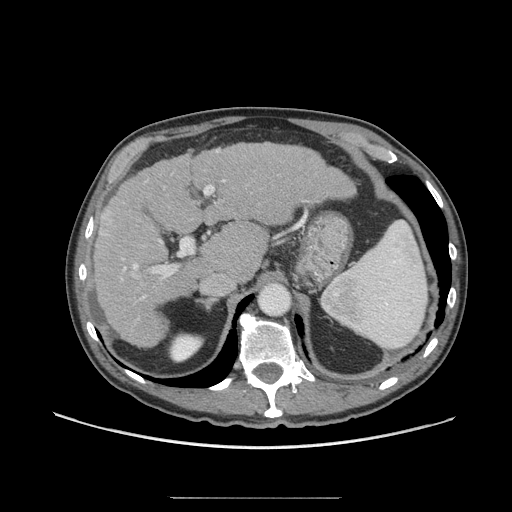
Contrast-enhanced abdominal CT (liver protocol), one axial slice; slice 44 of 71 in the series (ordered by position); 140 kVp; soft-tissue window (W 400 / L 40 HU); 512 × 512 image matrix, field of view 400 × 400 mm. From the clinical record (not read from this slice): diagnosis: hepatocellular carcinoma (patient treated with transarterial chemoembolisation; whether this scan precedes or follows treatment is not stated here); TNM stage (as recorded): Stage-I; Child-Pugh class: A; tumour differentiation: well differentiated; tumour nodularity: uninodular.
Annotated regions visible in this slice (semi-automatic segmentation, software-assisted and operator-edited):
- liver parenchyma outside the tumour (the mass and vessels are separate outlines, so this box may not span the whole liver): bounding box <92,142,354,346> (left, top, right, bottom; pixels)
- mass: <99,215,116,236>
- liver vessels: <122,150,225,298>